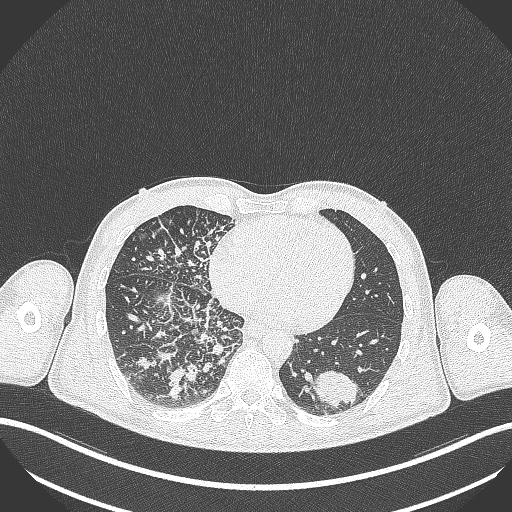
Chest CT, one axial slice; slice 106 of 348 in the series (ordered by position); lung window (W 1500 / L -600 HU); 1 mm slice thickness; 512 × 512 image matrix, field of view 400 × 400 mm. Patient: male, 49 years. Case-level facts recorded for this patient, not image findings: clinical TNM (as recorded): T2b N1 M0.
Structures marked on this image (rectangle marked by the reading radiologist):
- lung tumour (recorded histology: adenocarcinoma): box from (x=312, y=367) to (x=362, y=406) px